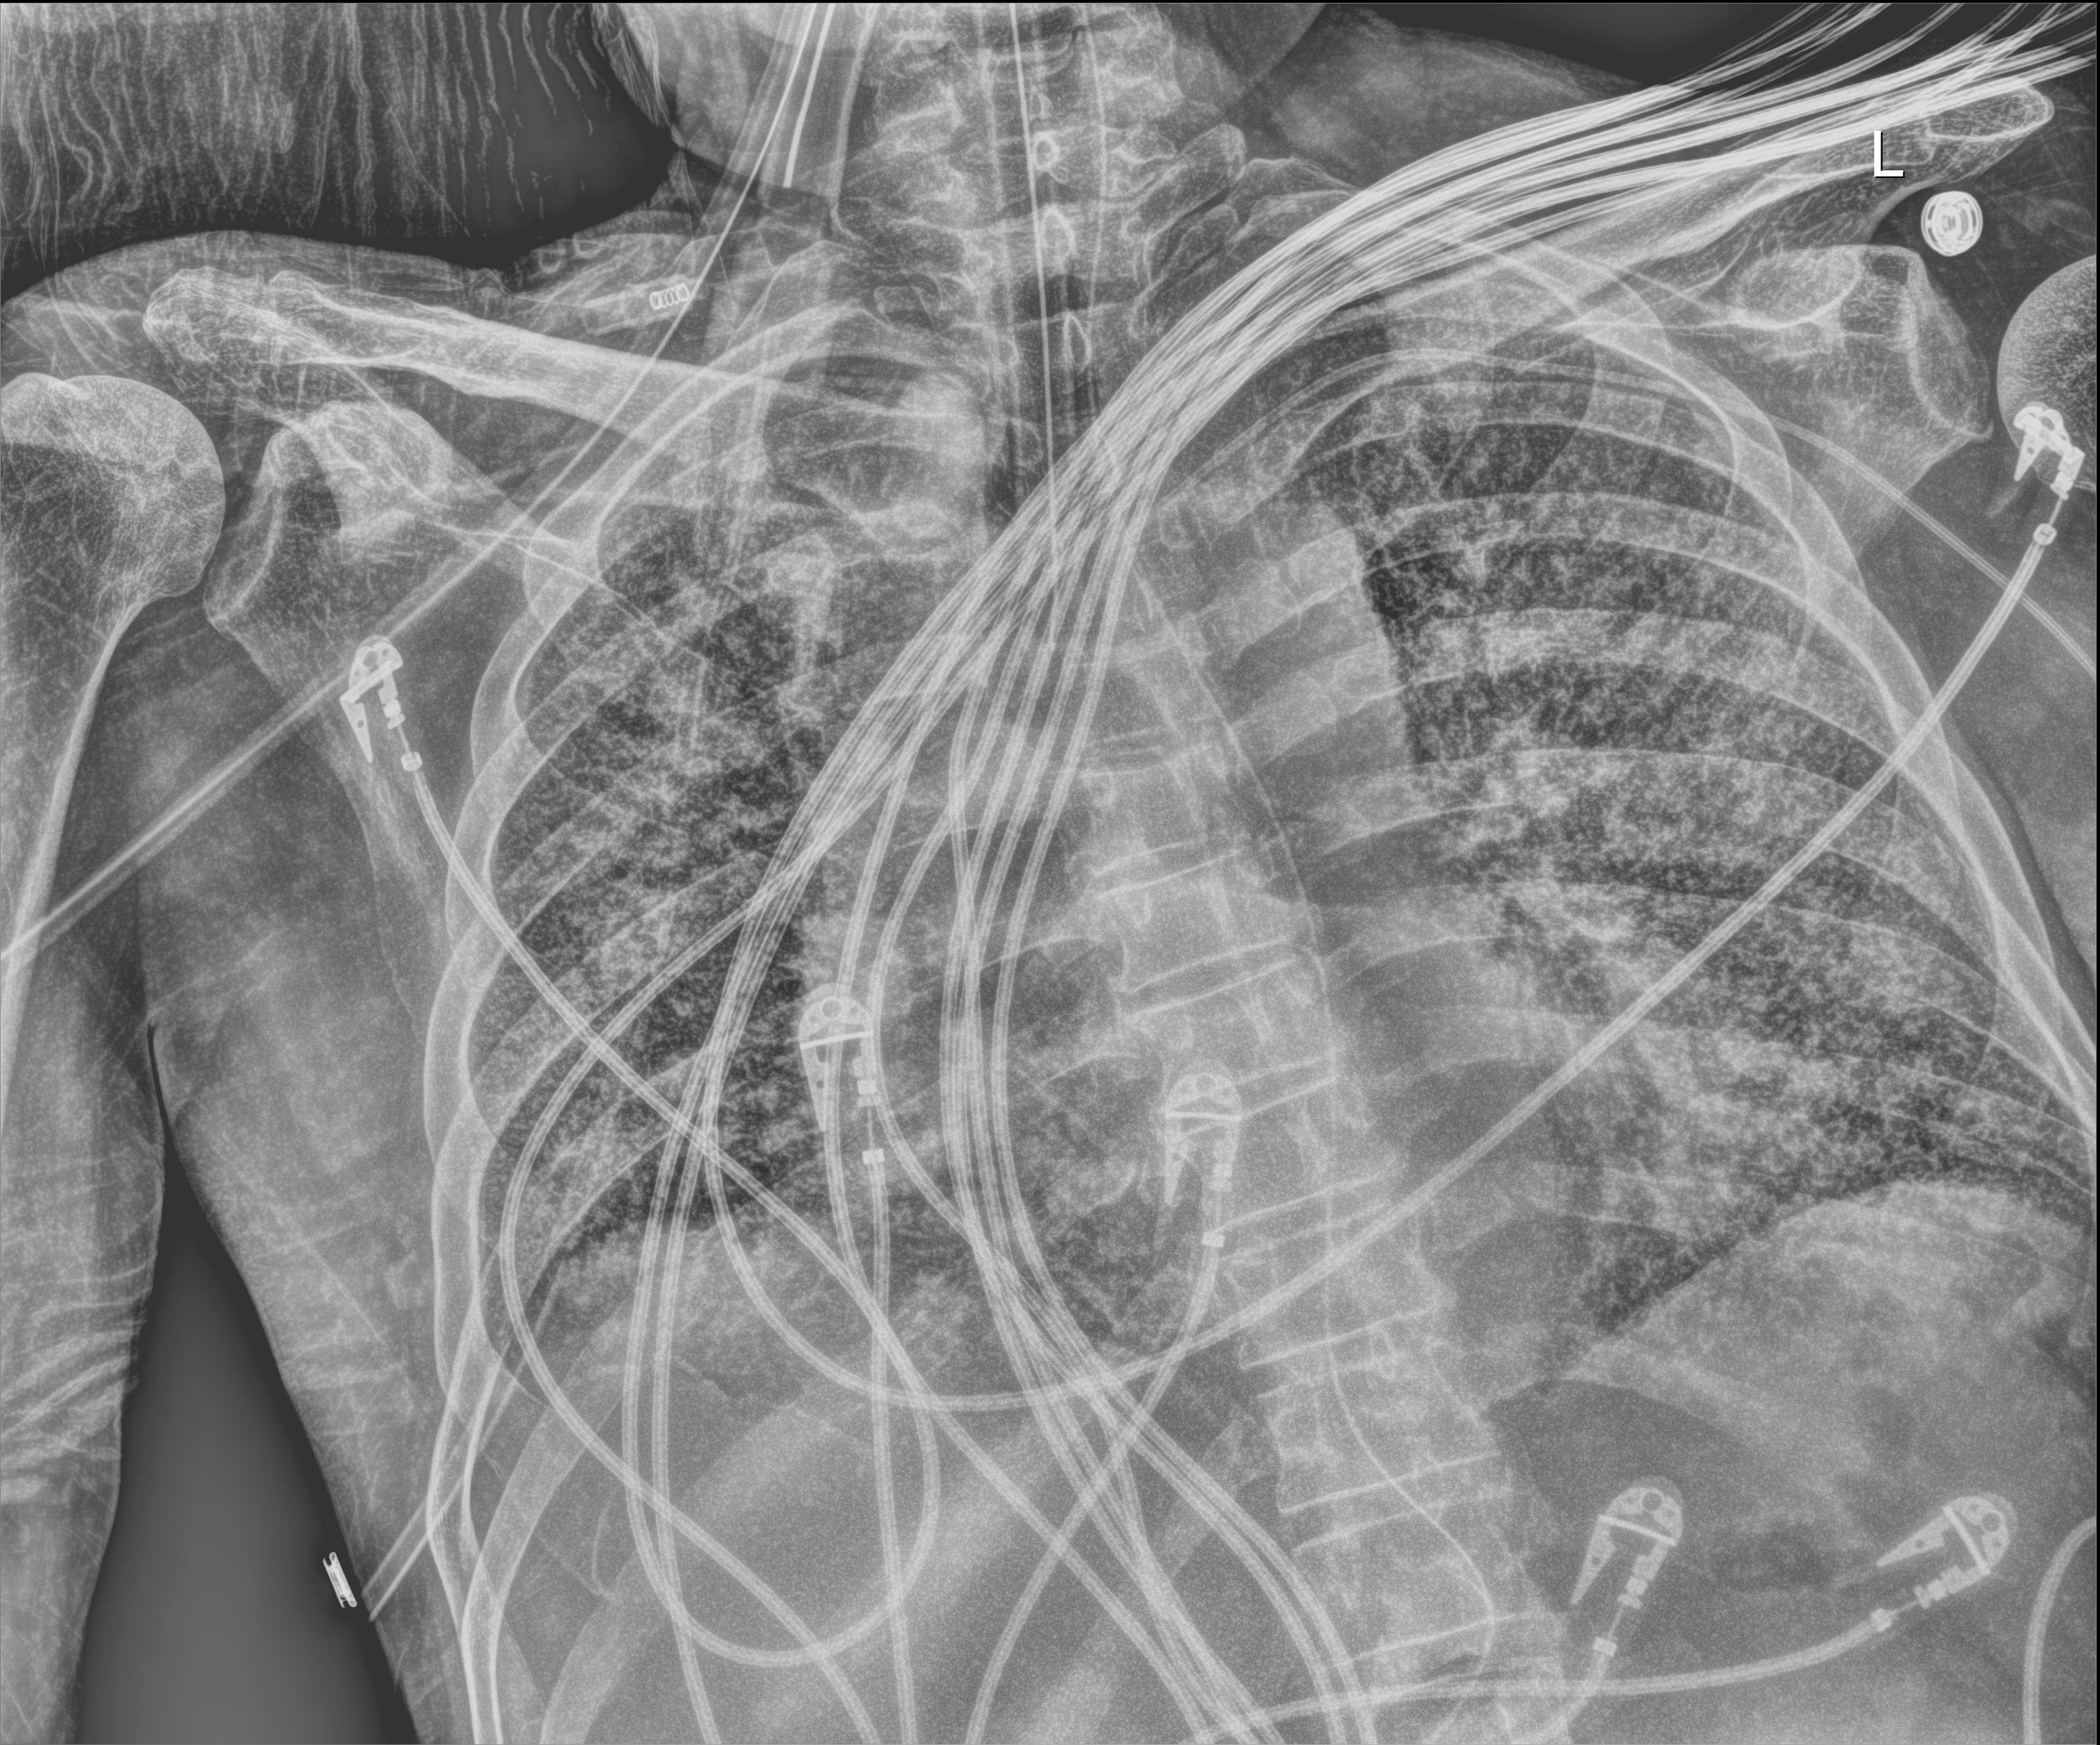
Chest X-ray; anteroposterior (AP) projection. Patient hospitalised with COVID-19; male, aged 60–74 years.
From the hospital-stay record, not from the radiograph (when in the stay this image was taken is not recorded):
- admitted to intensive care during this hospital stay: yes
- mechanically ventilated during this hospital stay: yes